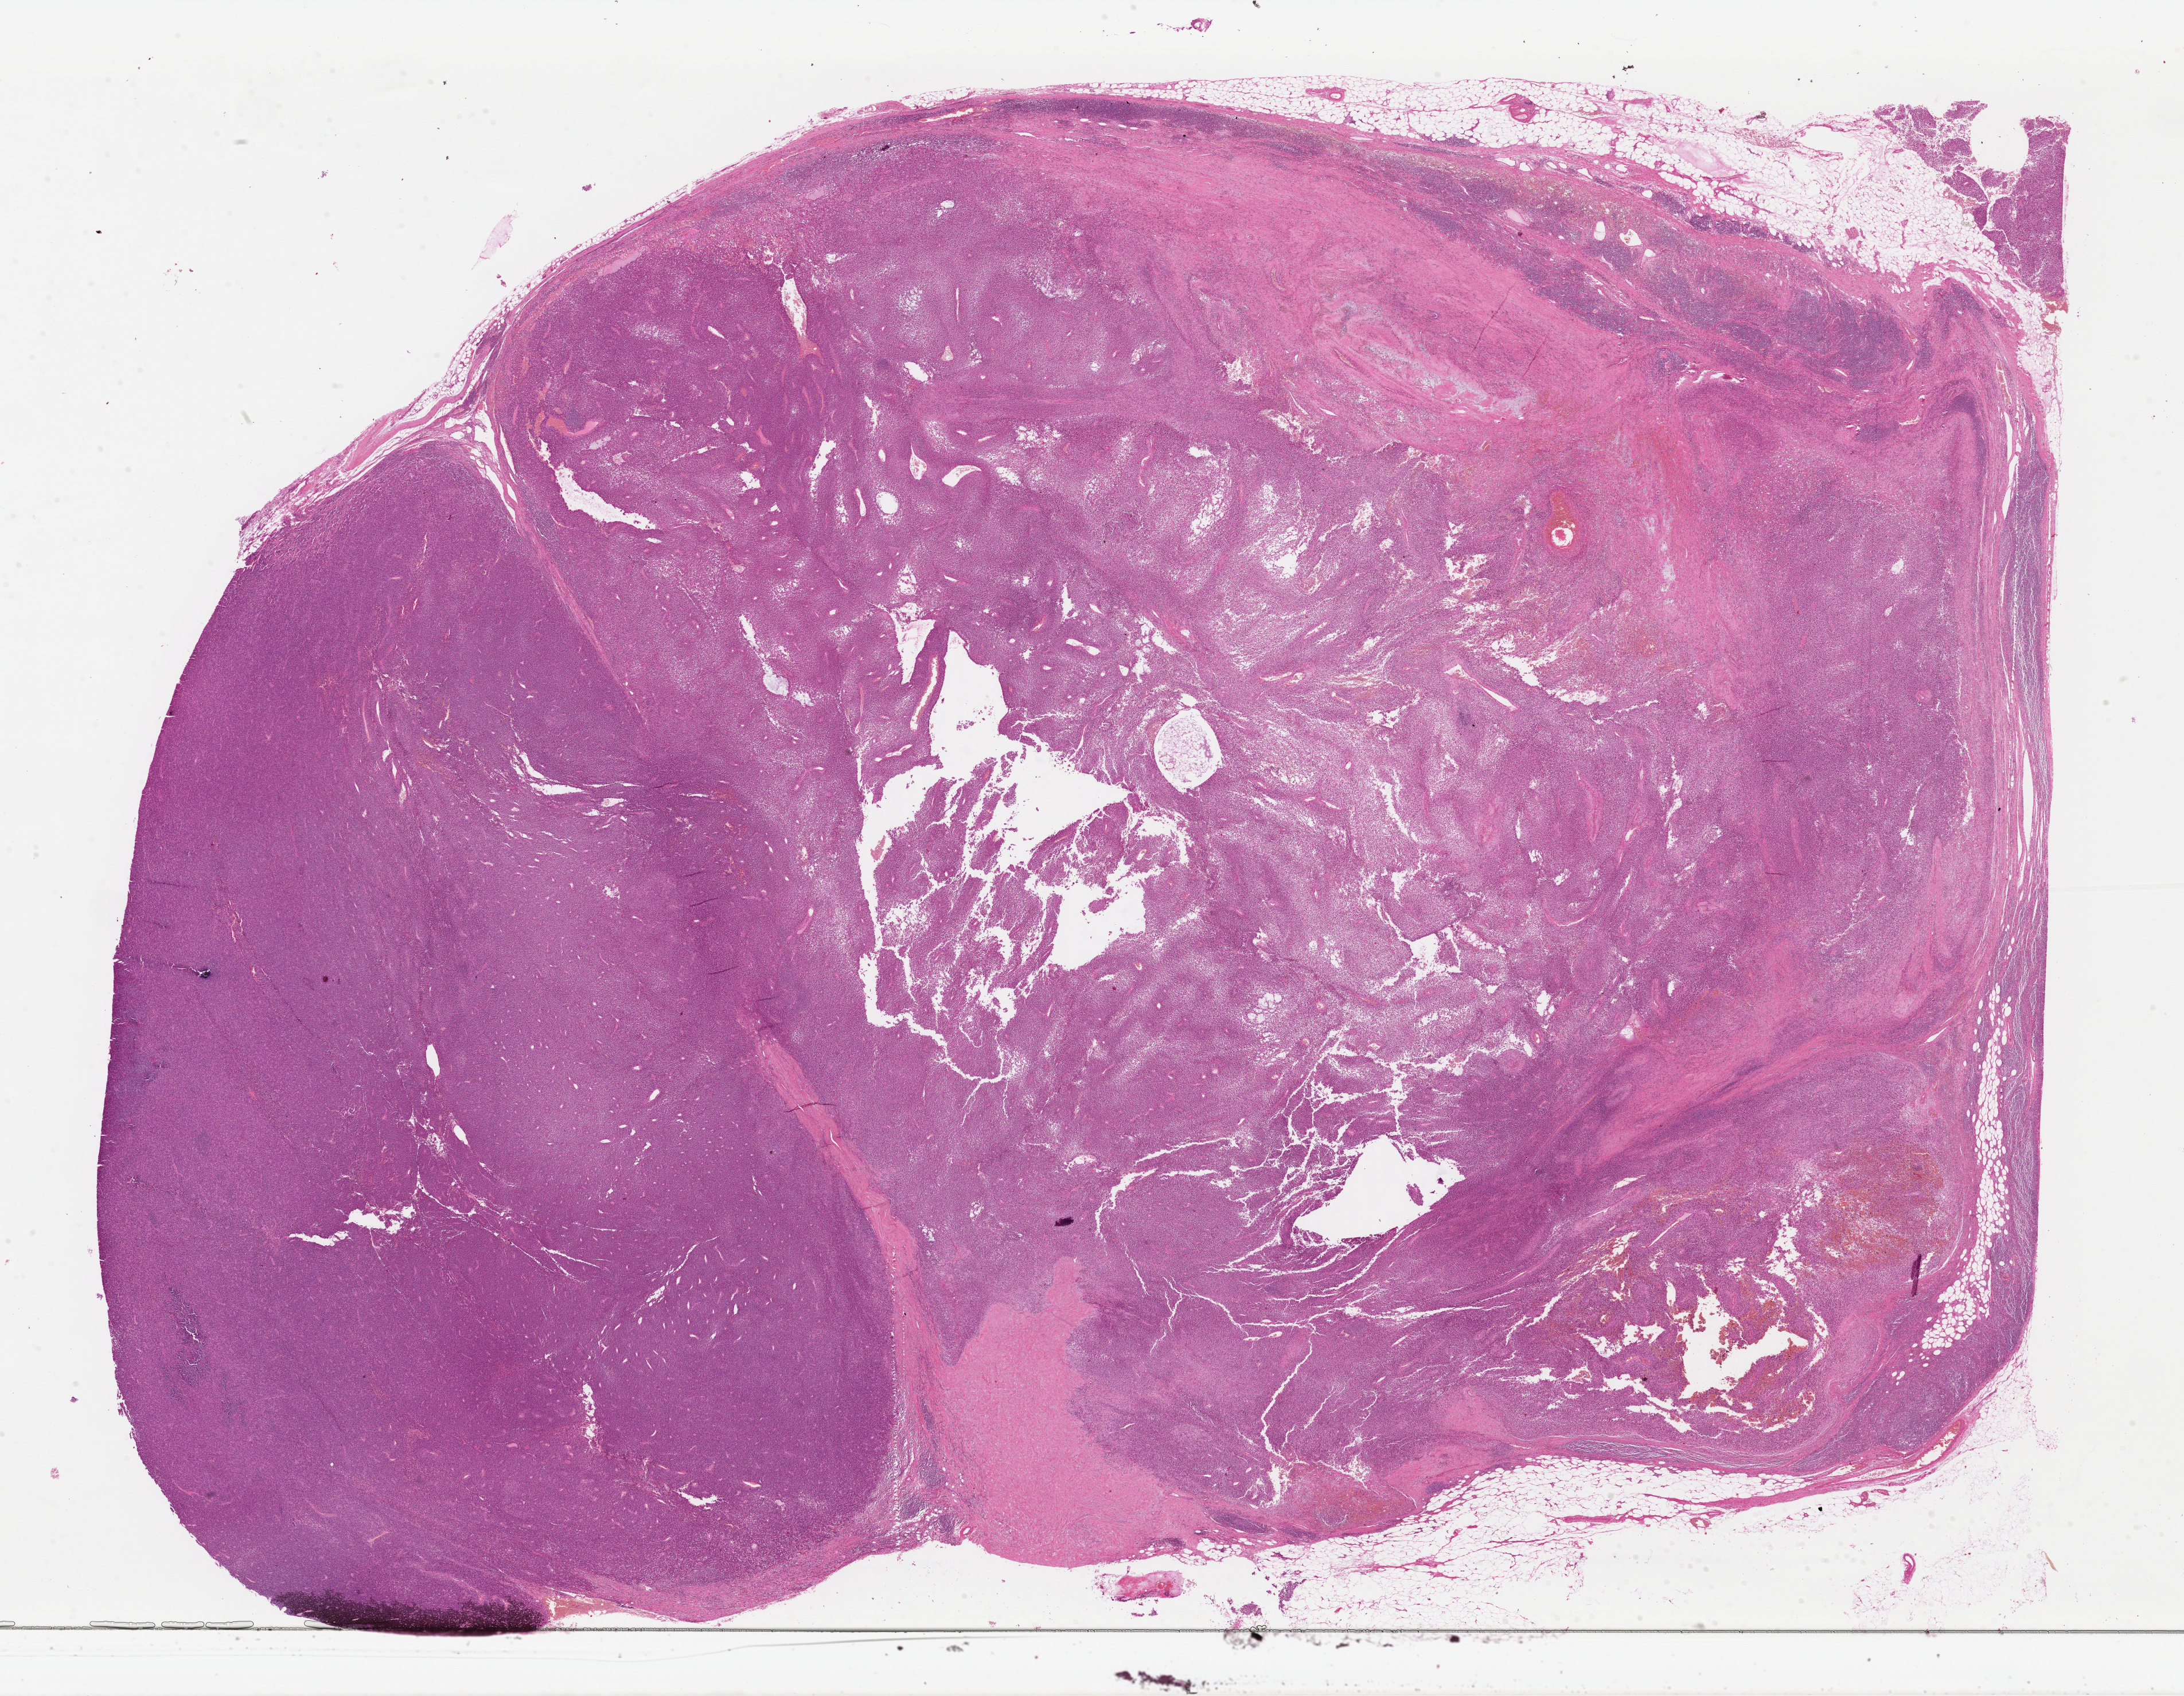
Digitized H&E-stained tissue section (whole slide) — low-resolution overview of the scanned area, about 29.9 x 23.2 mm. Formalin-fixed paraffin-embedded (FFPE) diagnostic section. Metastatic tumour sample, sampled site: lymph nodes of axilla or arm. Male patient; age at initial diagnosis 72 years.
This section: metastatic tumour tissue. Patient diagnosis: Malignant melanoma, NOS.